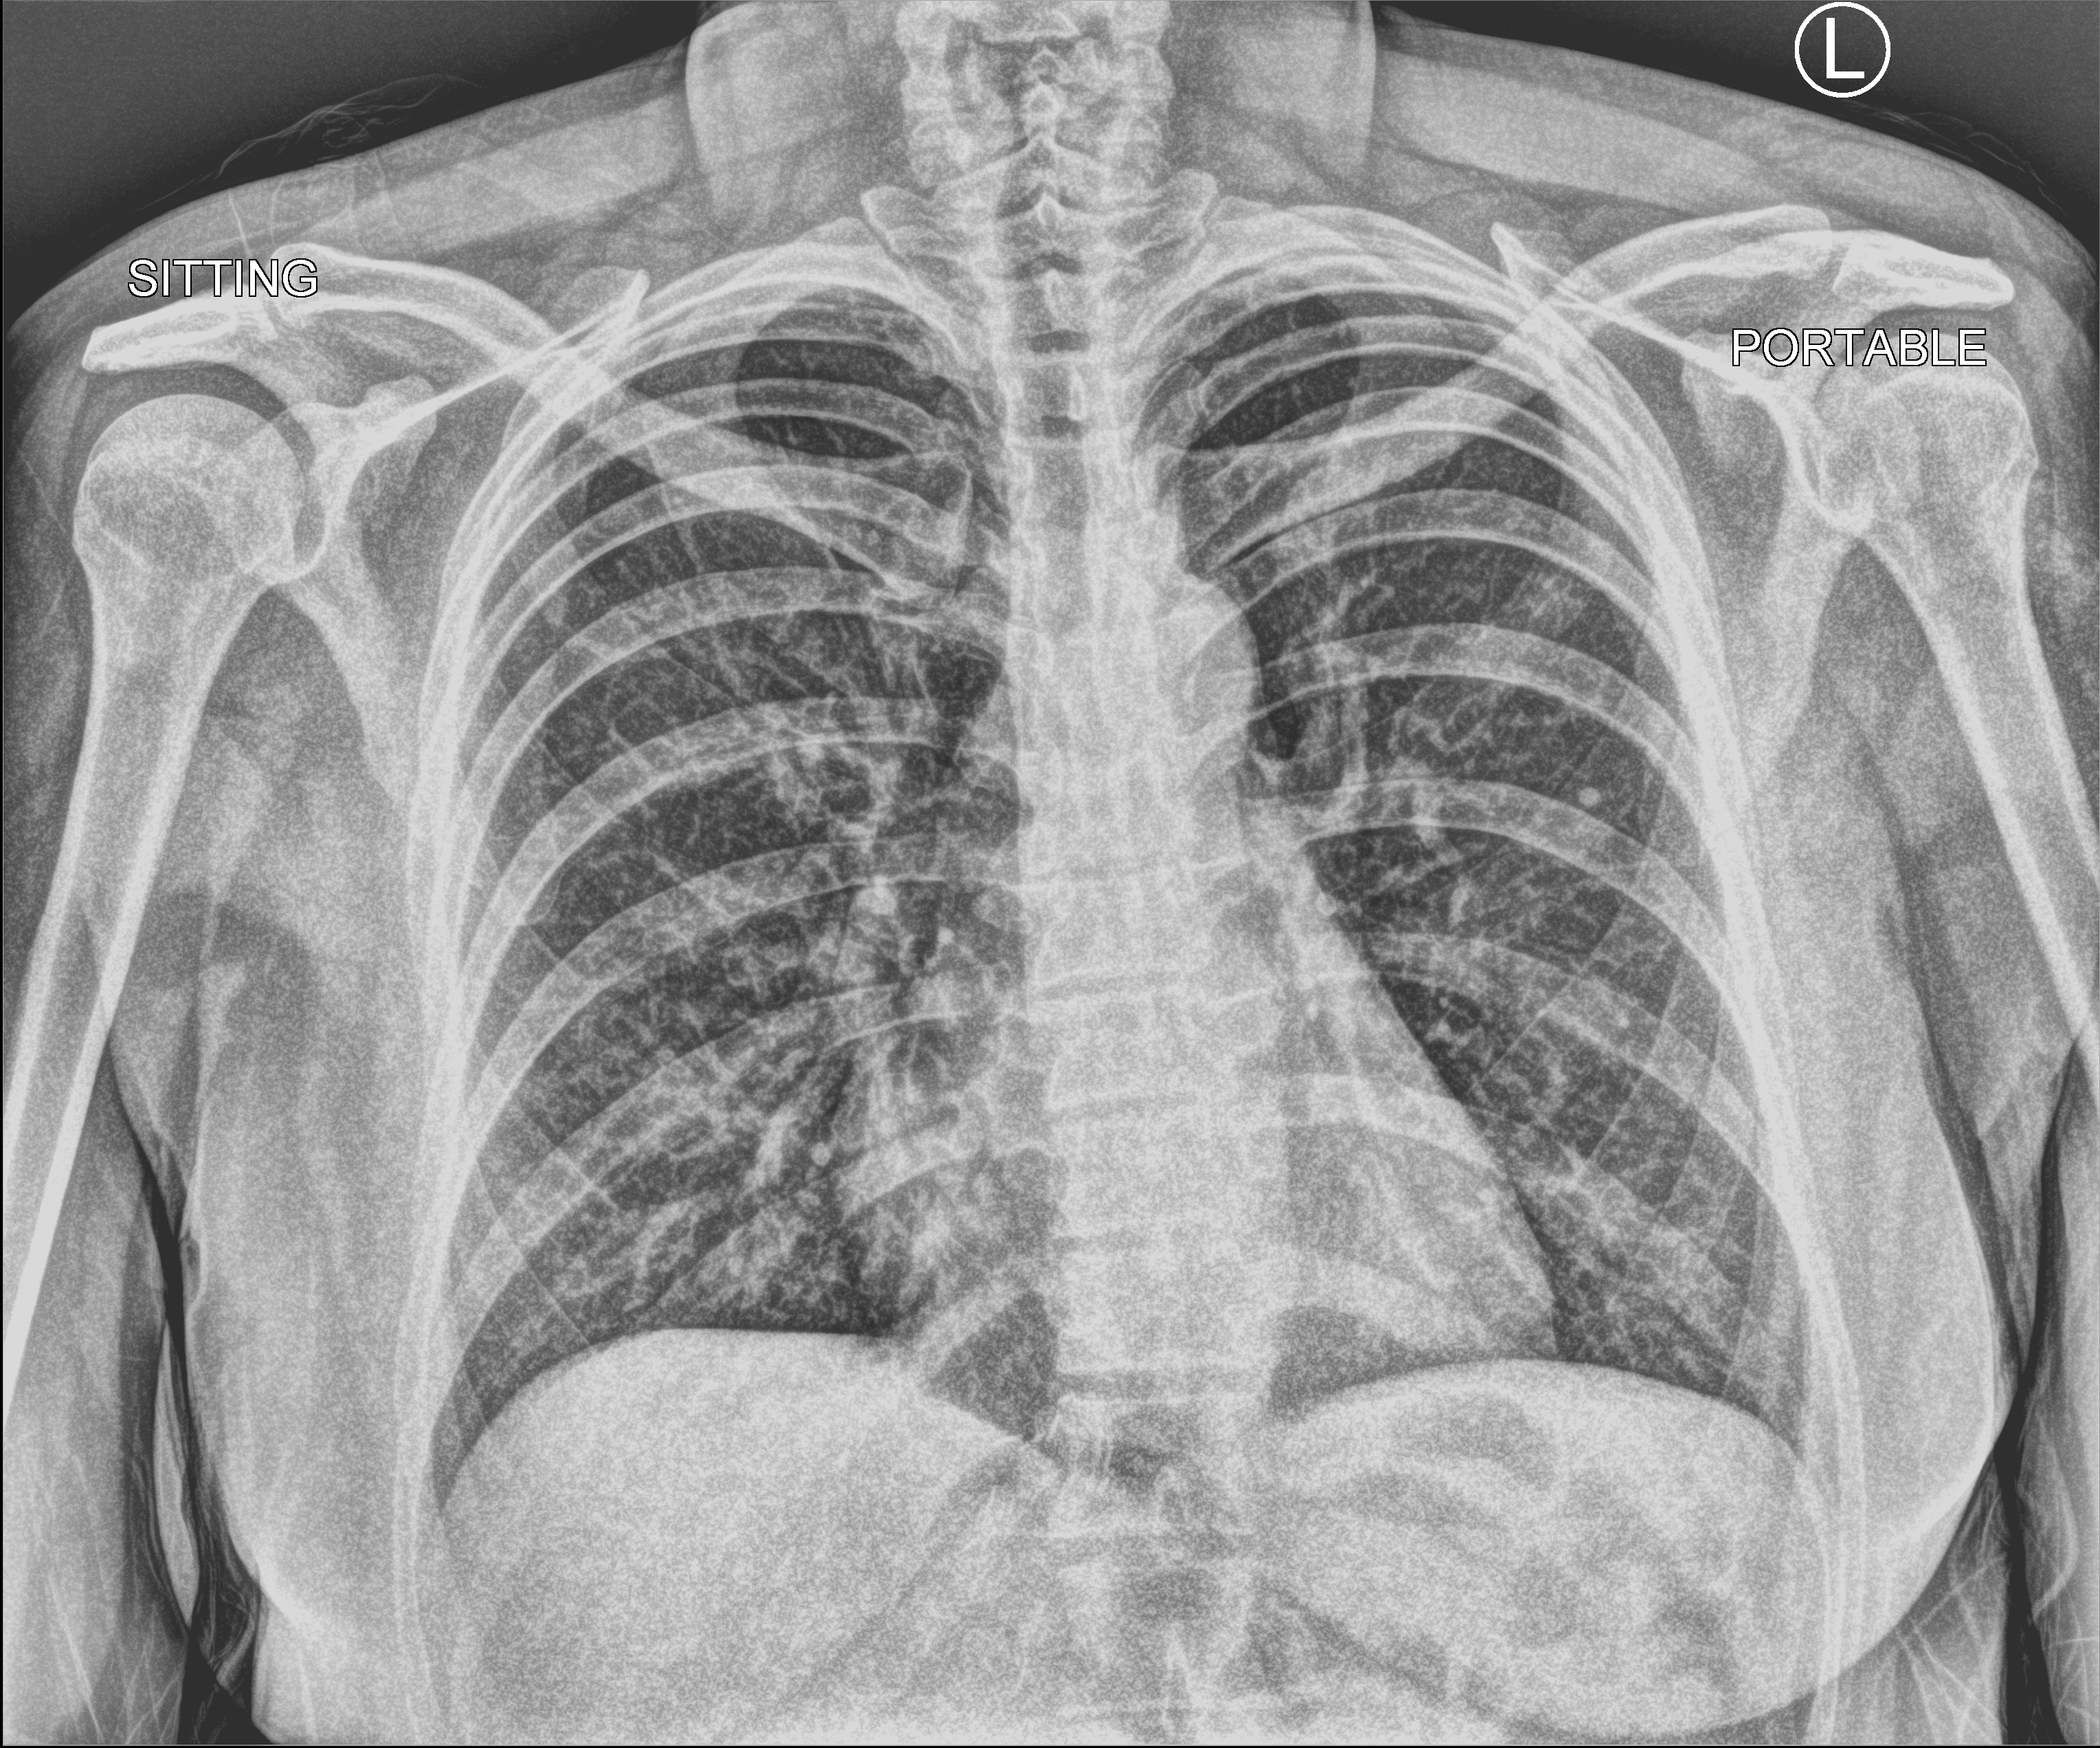
Bedside chest radiograph (computed radiography), anteroposterior (AP) projection. Patient hospitalised with COVID-19; female, aged 18–59 years.
Admission-level facts for this patient (not findings on this image; timing relative to this image not recorded): diabetes (admission record): no; length of hospital stay: 1 day; hypertension (admission record): no.